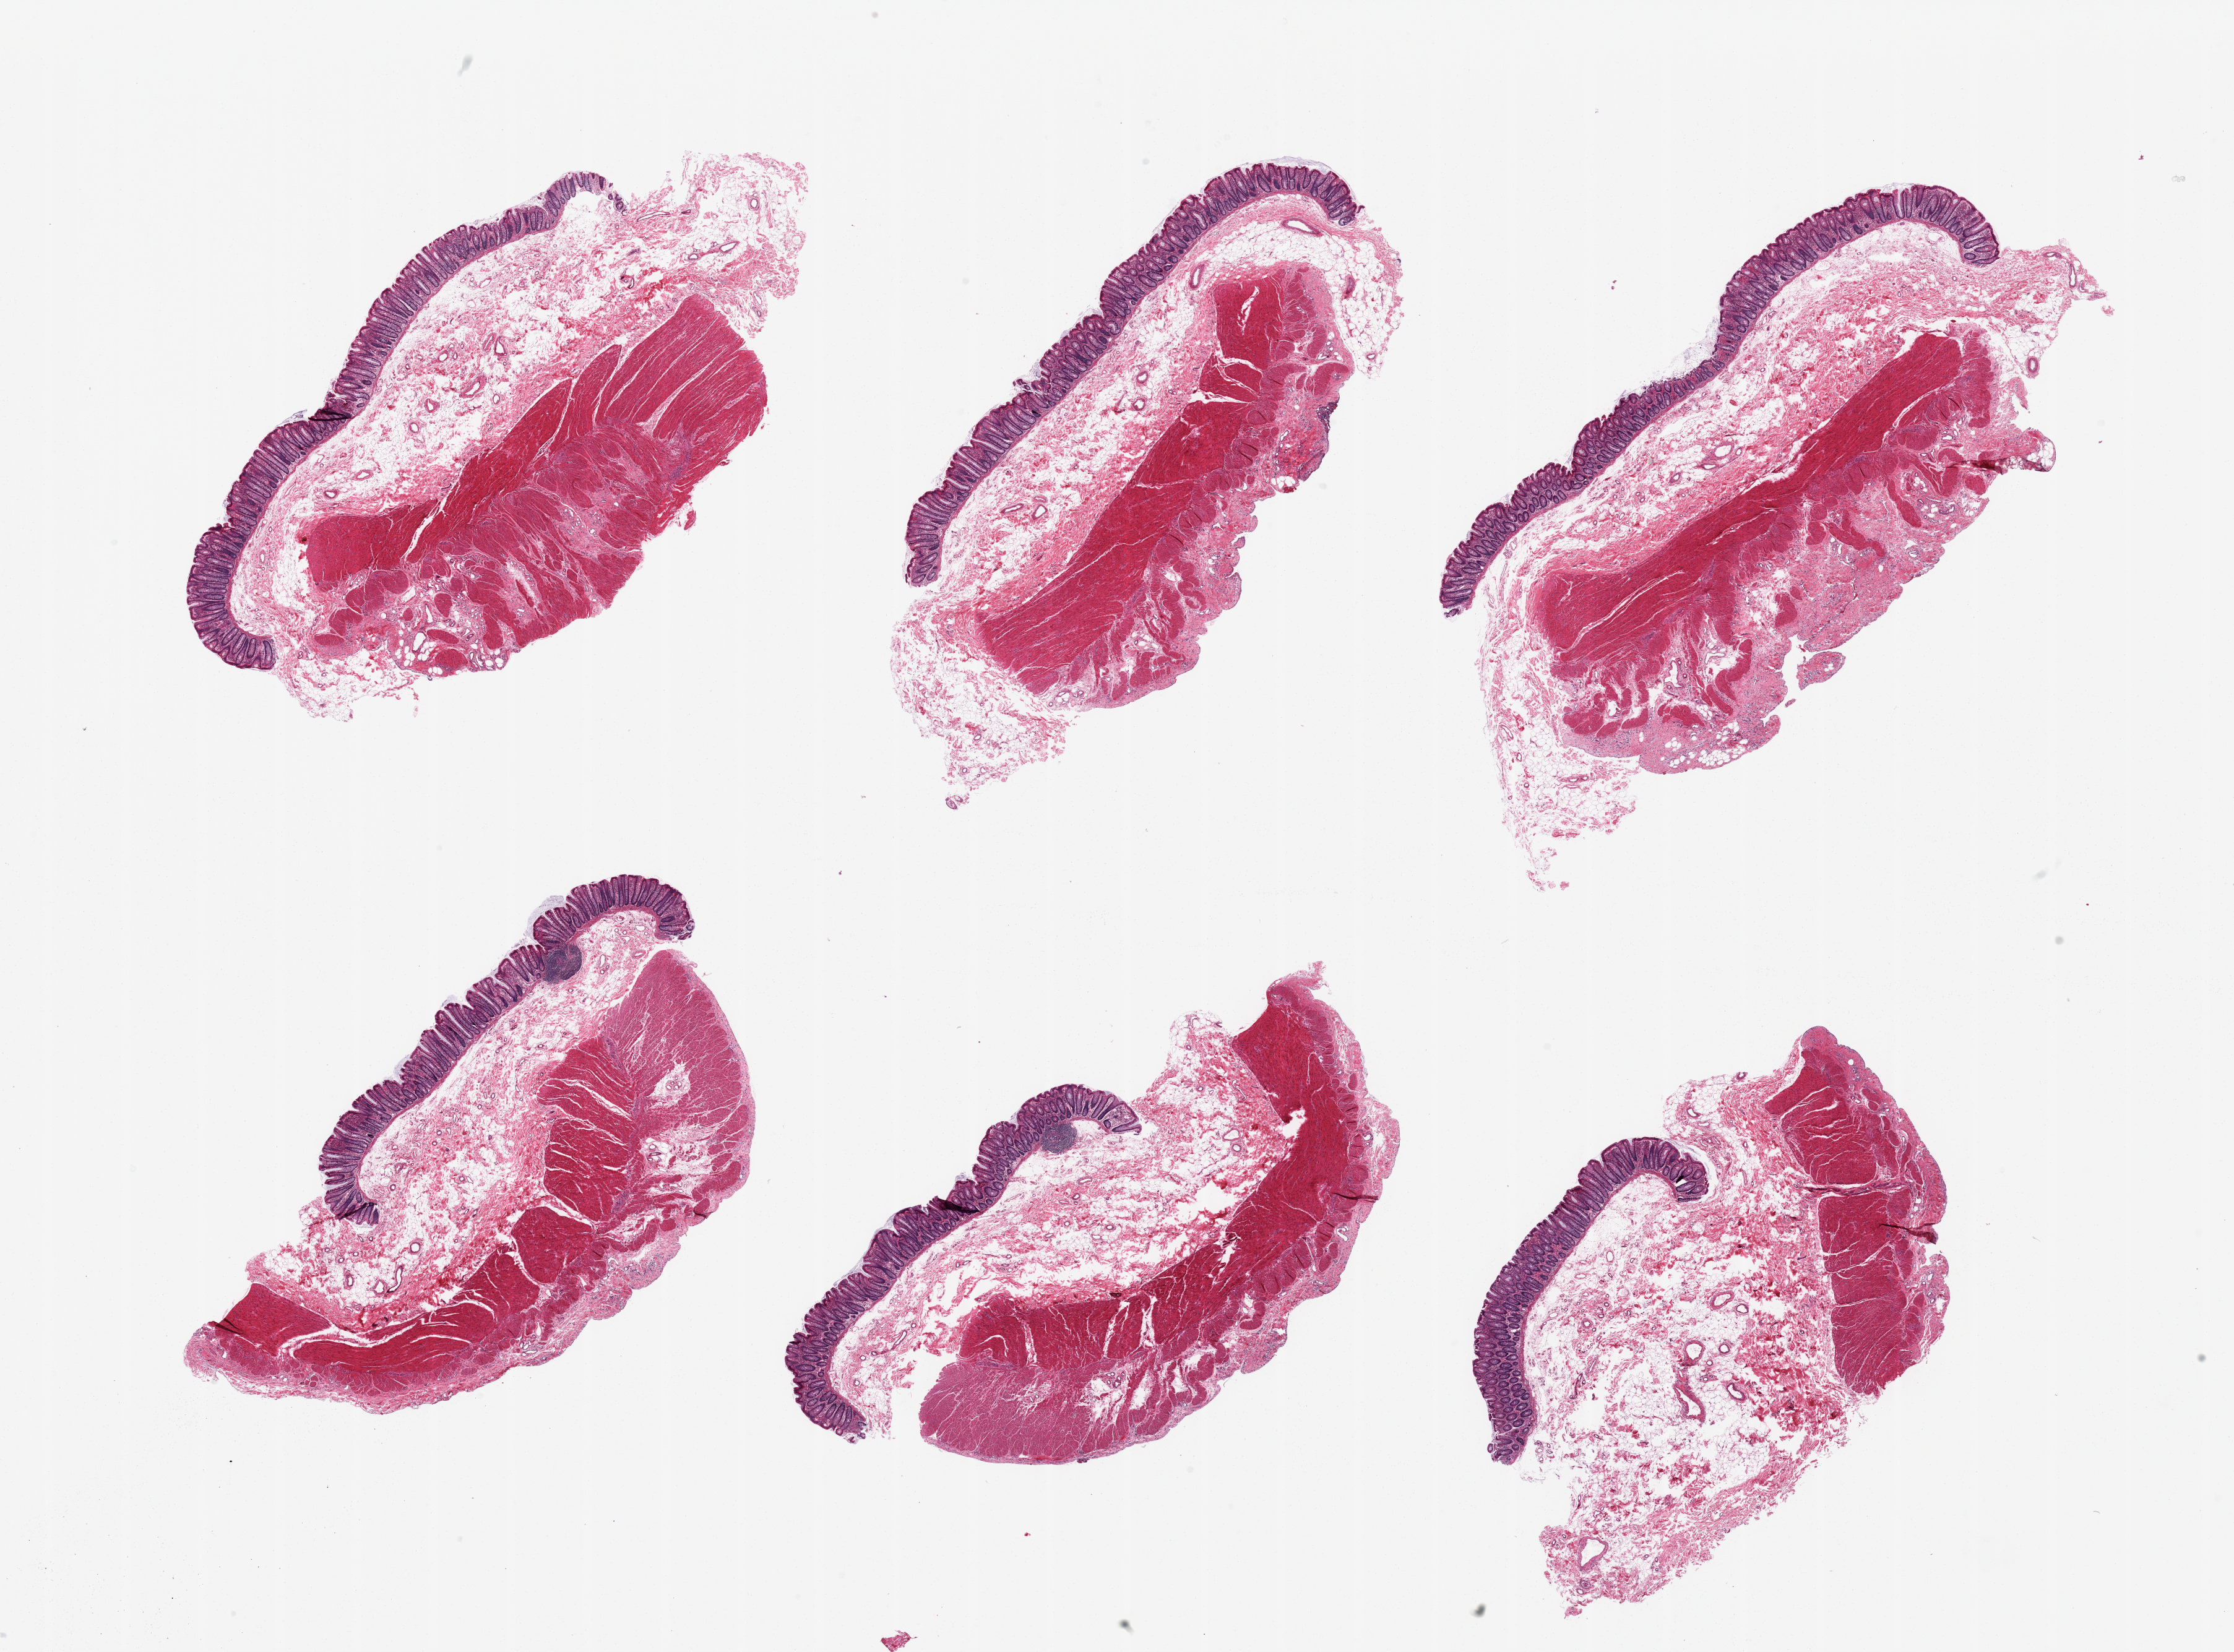
Whole-slide image, H&E stain, brightfield, low-resolution overview of the scanned area, about 28.5 x 21.1 mm, PAXgene-fixed paraffin-embedded (PFPE) section, sampled site (target tissue): transverse colon, tissue donor sample. Donor sex: male.
Reviewer comment on this tissue sample: 6 pieces; well preserved and dissected mucosa and muscularis.